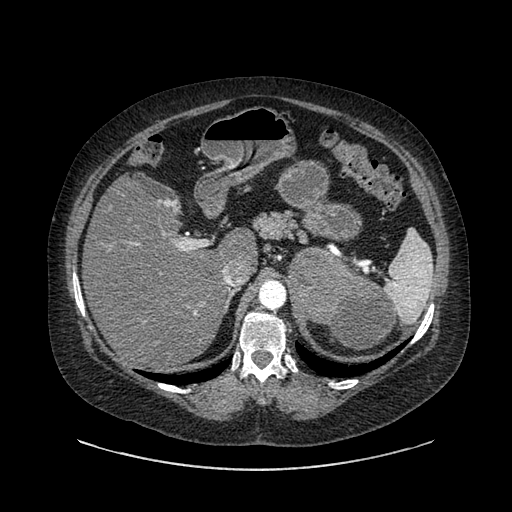
Contrast-enhanced abdominal CT, one axial slice. Slice 602 of 769 in the series (ordered by position). Reconstruction kernel SOFT. 120 kVp. Intravenous contrast given. Soft-tissue window (W 400 / L 40 HU). 0.62 mm slice thickness. 512 × 512 image matrix, field of view 460 × 460 mm. Patient: female, 61 years. From the clinical record (not read from this slice): diagnosis: adrenocortical carcinoma; tumour side: left adrenal; tumour size at pathology: 13 cm.
Annotated regions visible in this slice (semi-automatic segmentation, software-assisted and operator-edited):
- mass: box from (x=289, y=250) to (x=395, y=350) px